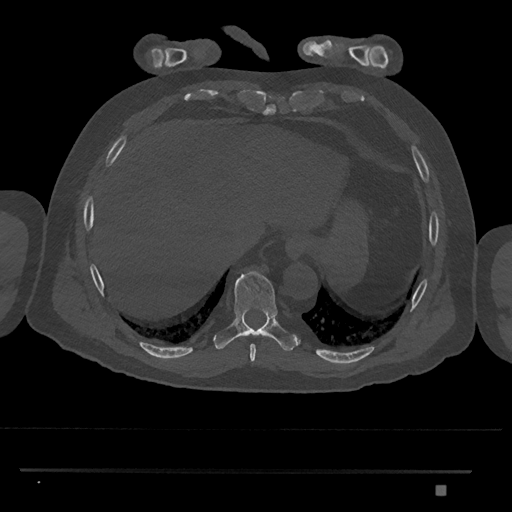
CT including the spine, one axial slice; slice 1064 of 1134 in the series (ordered by position); 120 kVp; bone window (W 1800 / L 400 HU); 0.5 mm slice thickness; 512 × 512 image matrix, field of view 429 × 429 mm. Male patient, age 65 years. From the clinical record (not read from this slice): primary cancer: prostate.
Outlined on this slice (semi-automatically segmented with operator editing):
- T8 vertebra: bounding box <250,344,256,363> (left, top, right, bottom; pixels)
- T9 vertebra: <214,271,301,351>